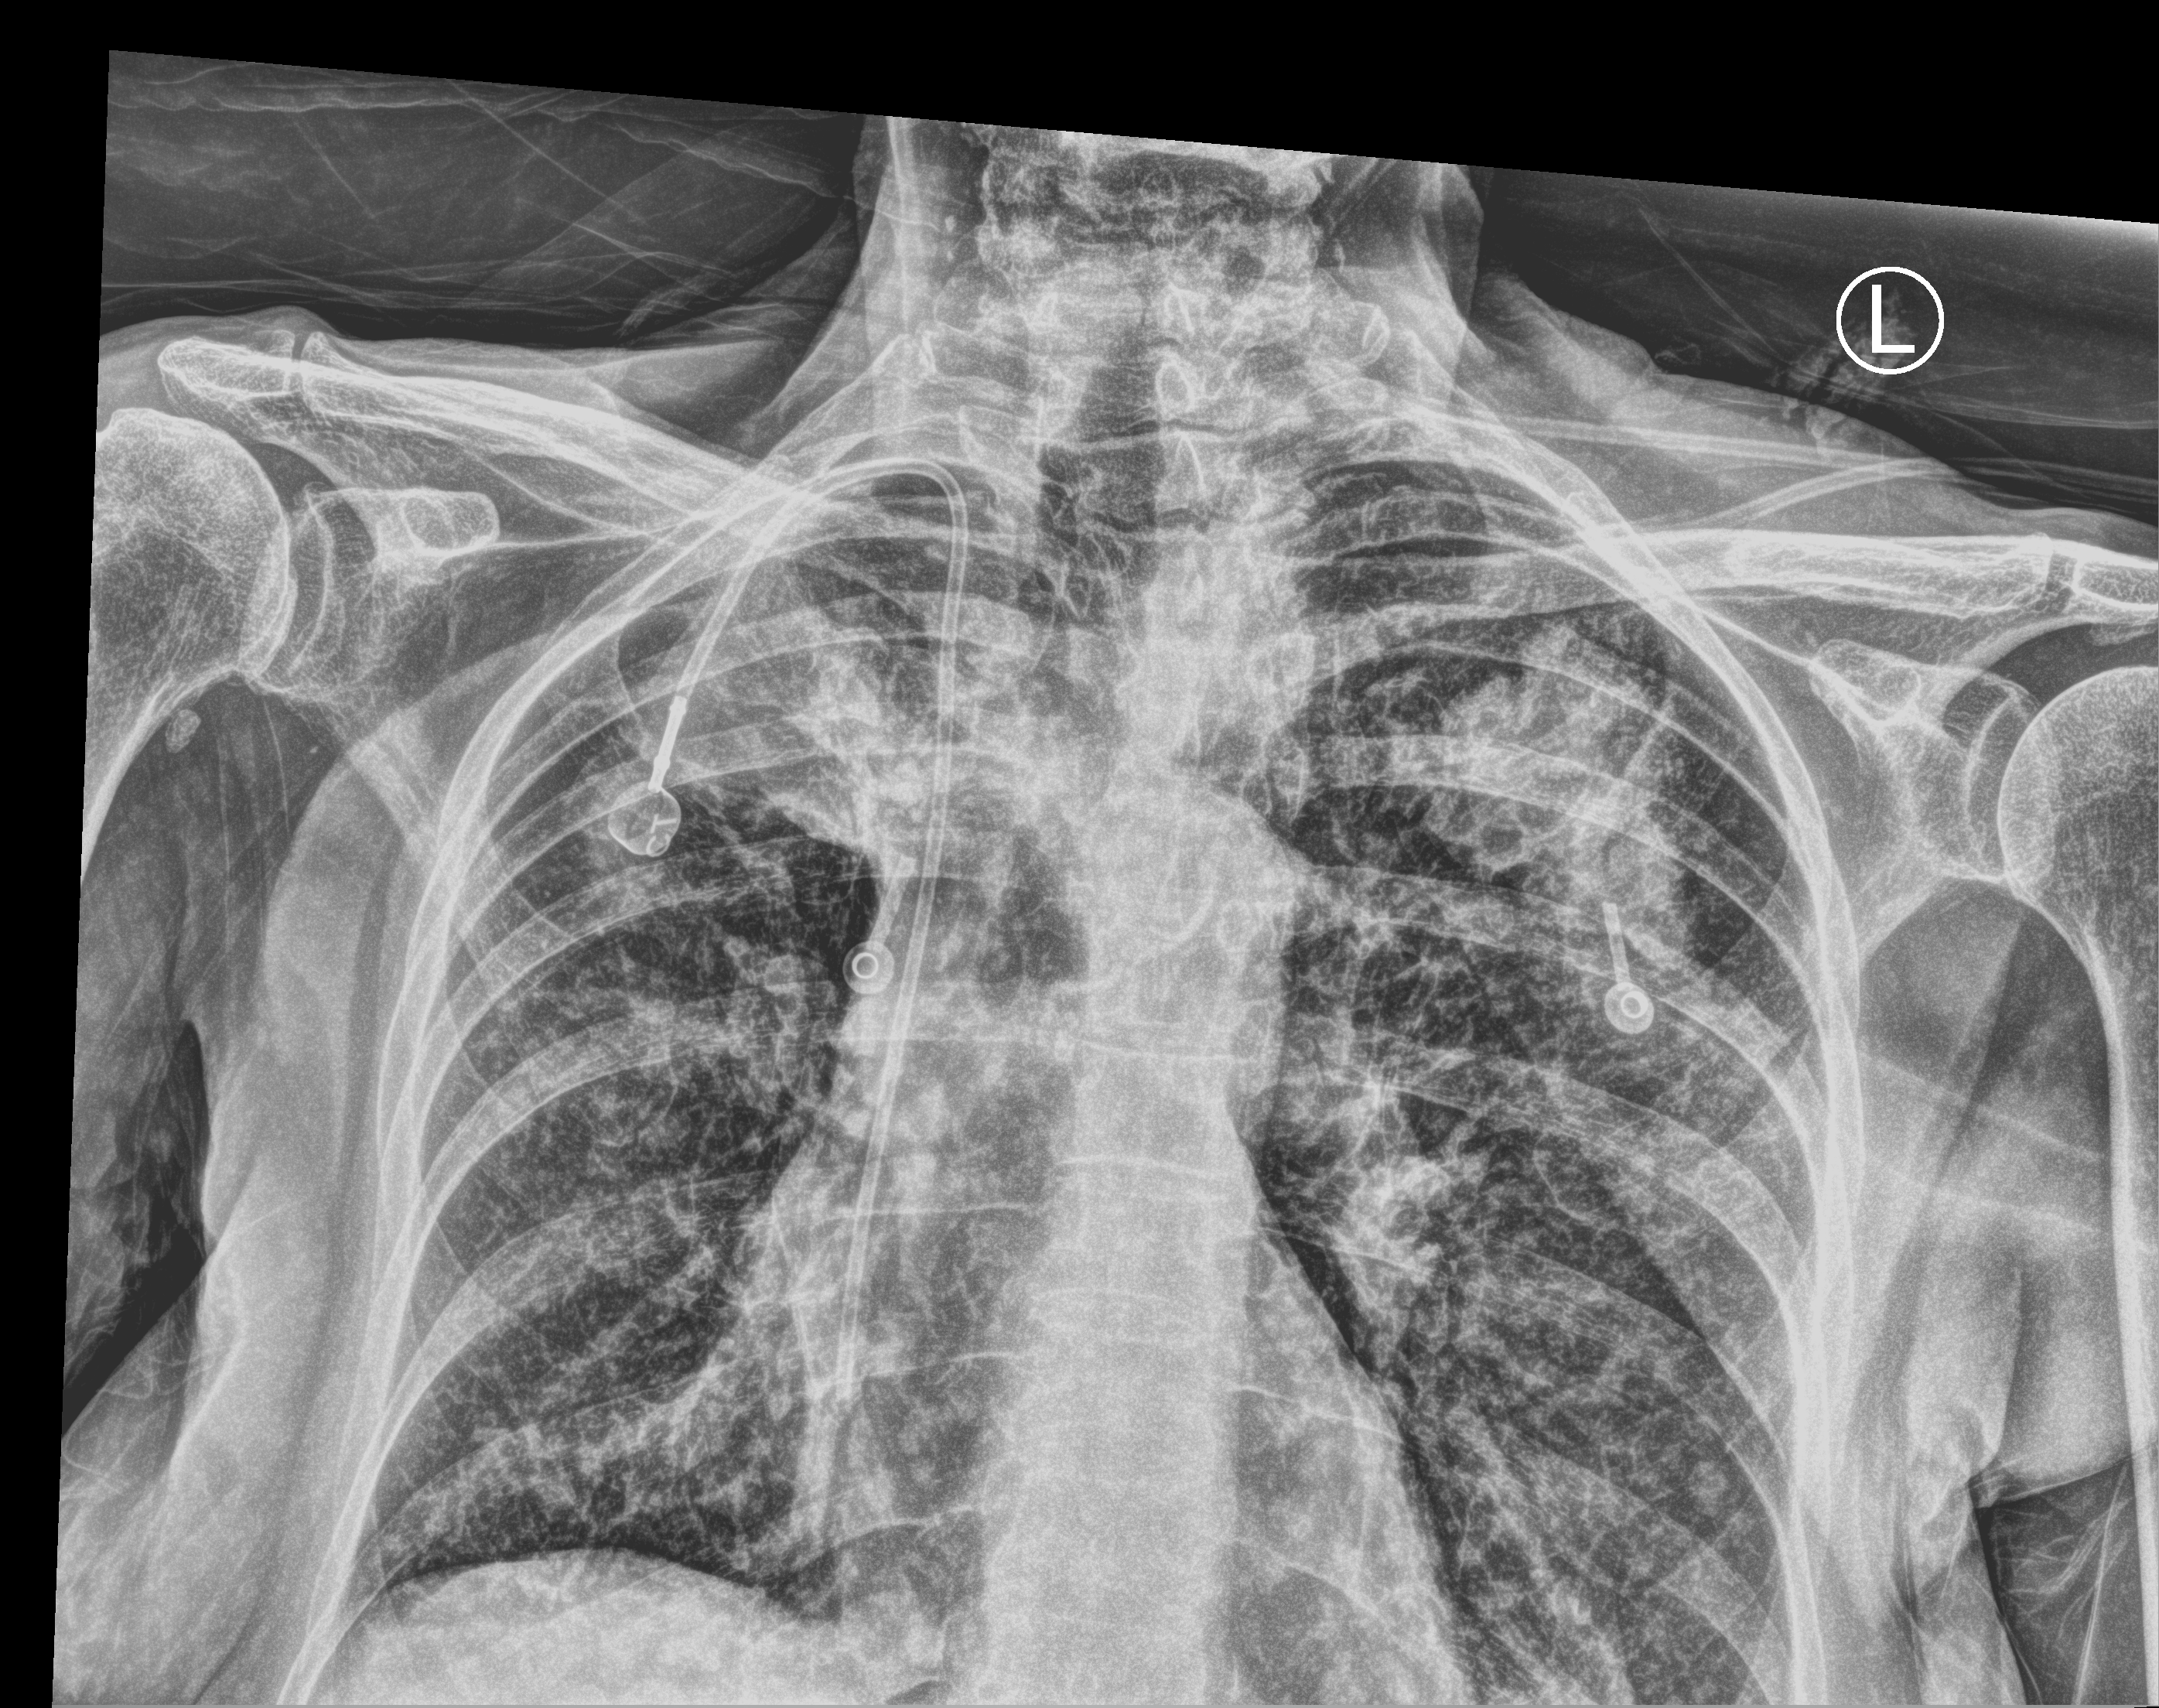
Bedside chest radiograph (computed radiography), anteroposterior (AP) projection. Female patient hospitalised with COVID-19, age 60–74 years.
Hospital-stay facts (about this admission, not read from this image; timing relative to this image not recorded):
- length of hospital stay: 8 days